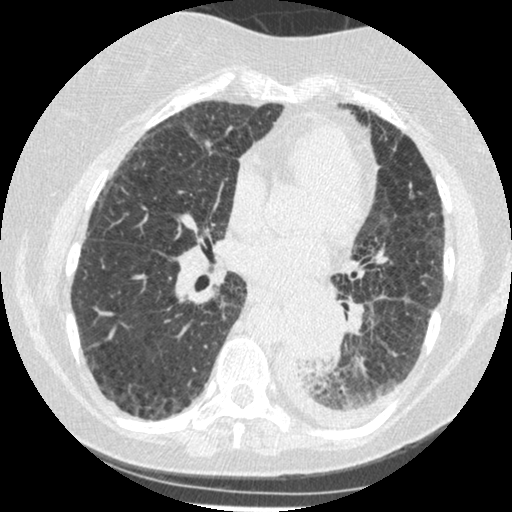
Low-dose screening chest CT, one axial slice; position 111 of 341 along the scan axis; 120 kVp; lung window (W 1500 / L -600 HU); 1.25 mm slice thickness; 512 × 512 image matrix, field of view 310 × 310 mm.
Structures marked on this image (manually delineated by an expert):
- lesion 1 (tumor, lower lobe of left lung): box from (x=285, y=302) to (x=339, y=364) px